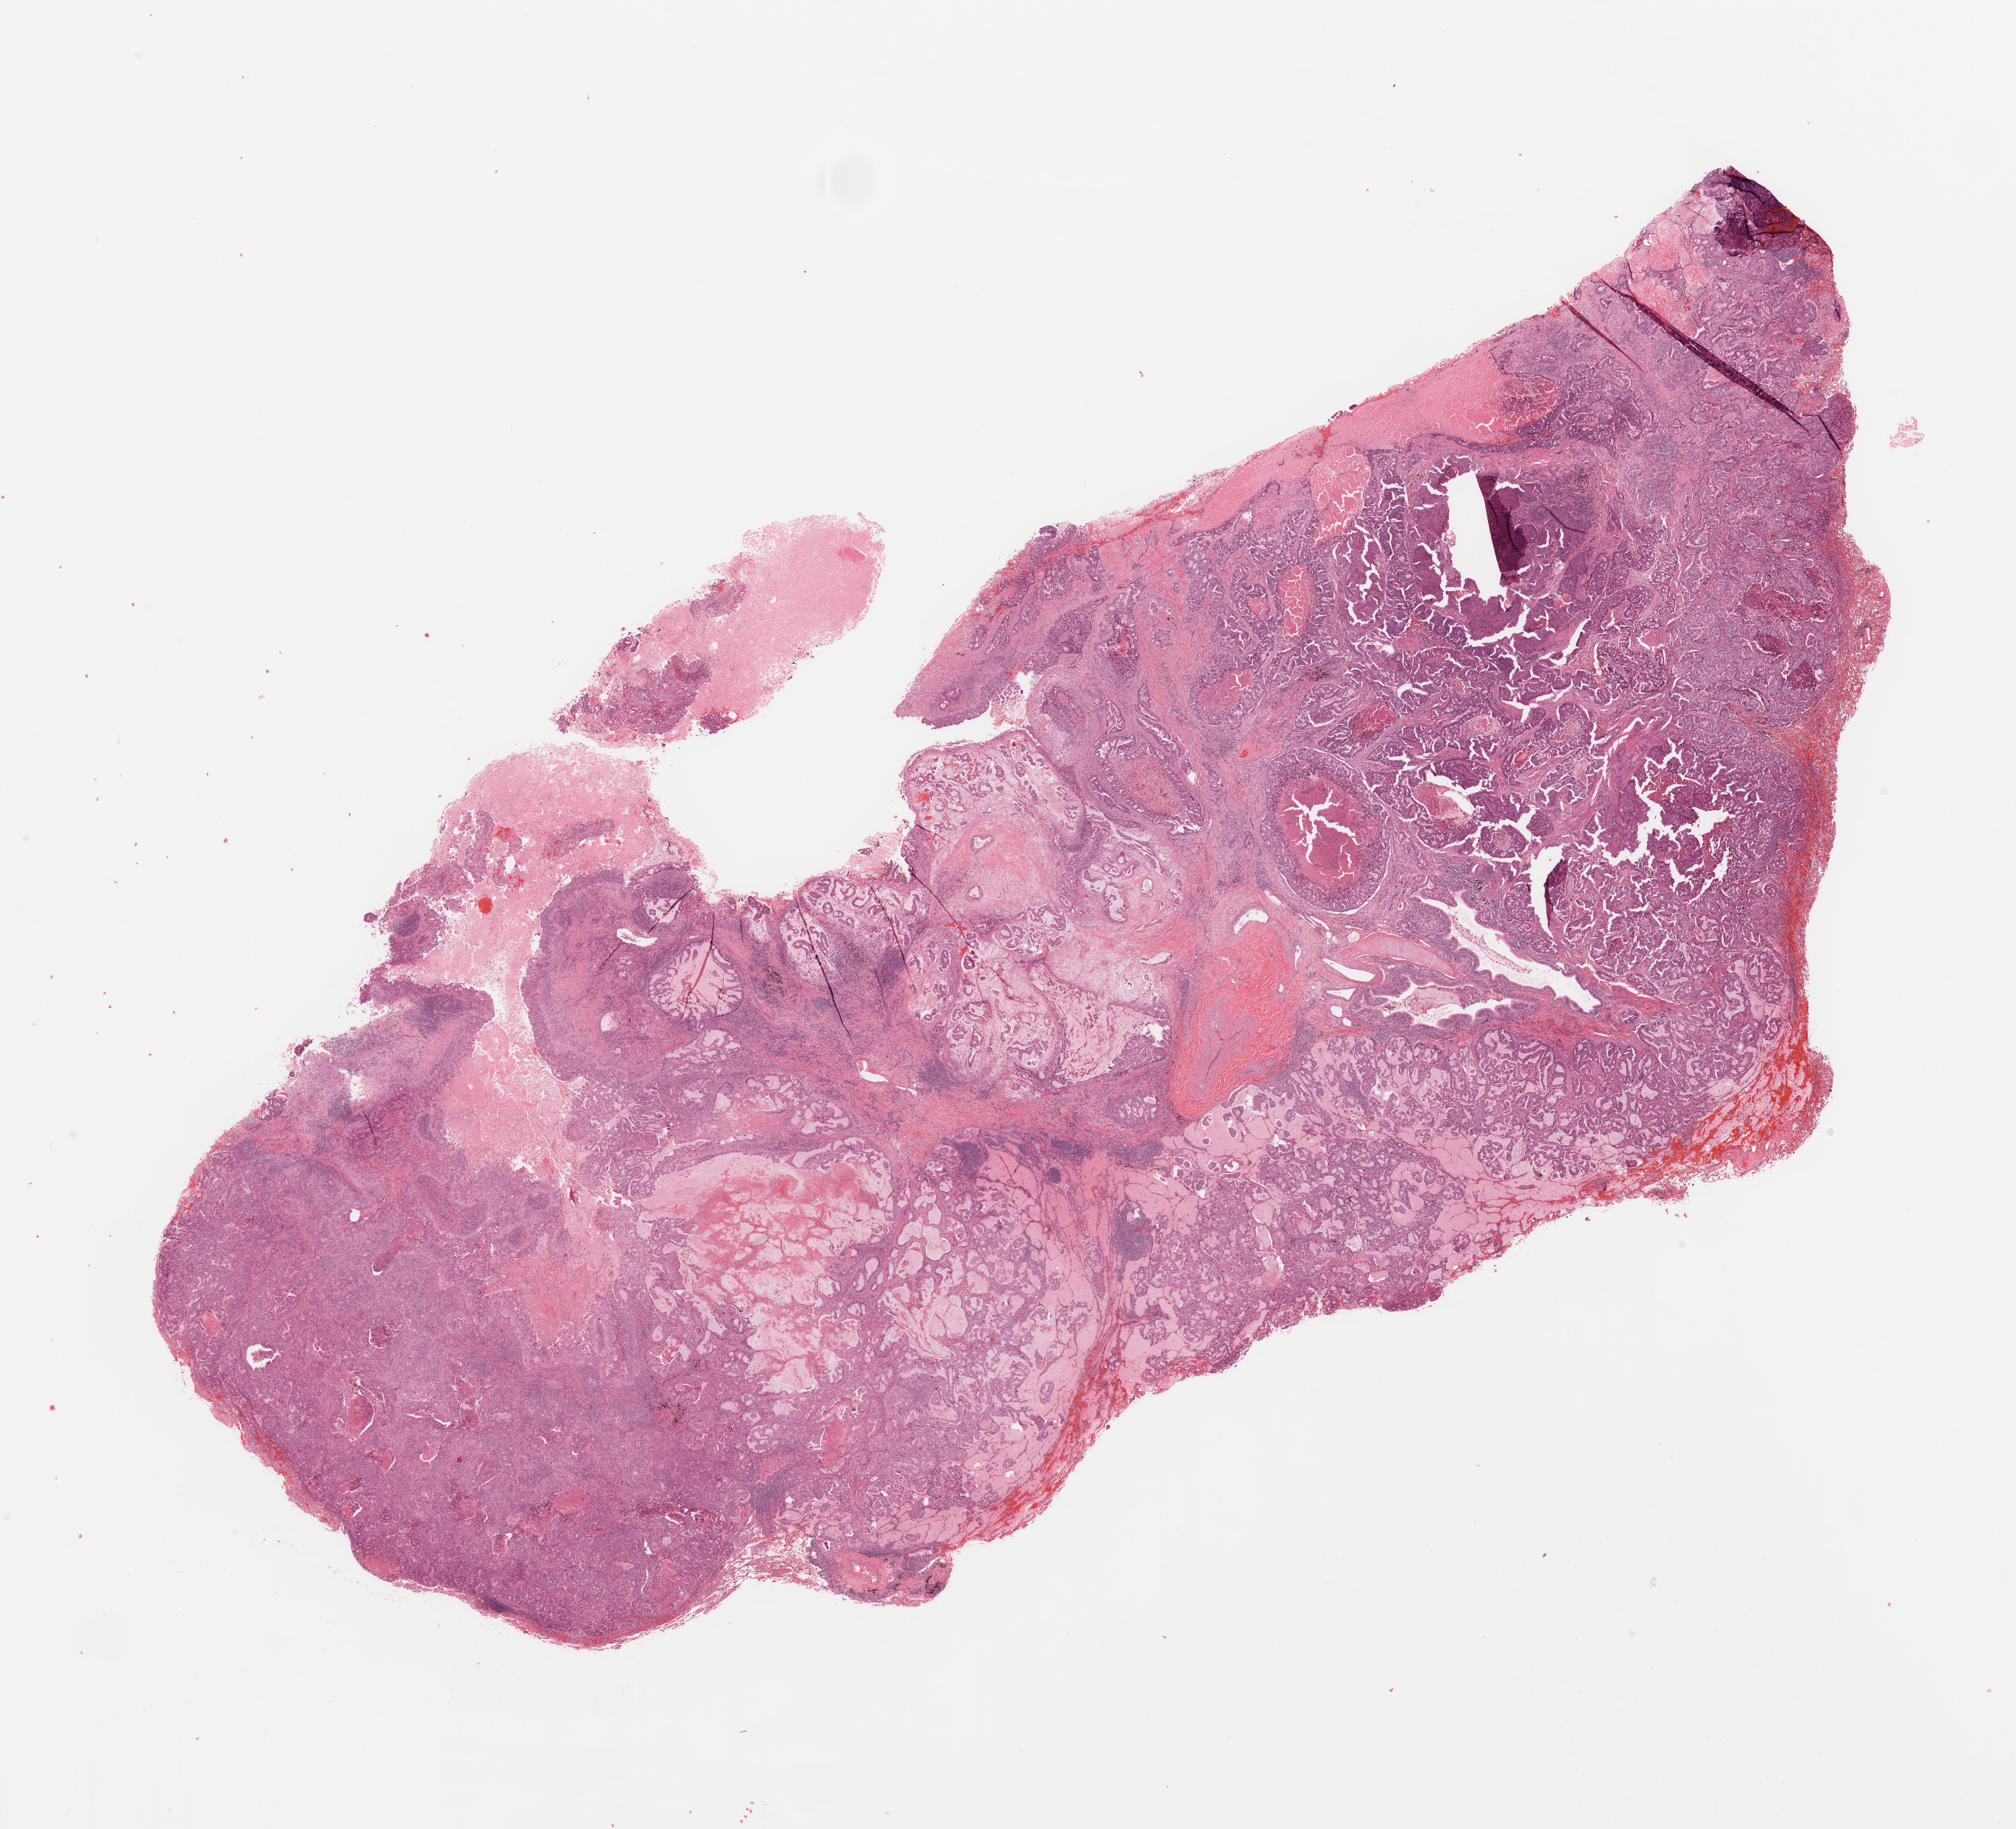
H&E-stained whole-slide image — low-resolution overview of the scanned area, about 21.7 x 19.6 mm (from a 20x scan); tumour tissue sample, sampled site: lung. Patient: male, age 40 years. Histologic grade: G2 (moderately differentiated). Composition of this section per pathologist review: tumour nuclei 70%, necrosis 20%.
* AJCC pathologic stage: IB
* diagnosis: Adenocarcinoma, NOS
* primary tumour site (as recorded): right lower lobe